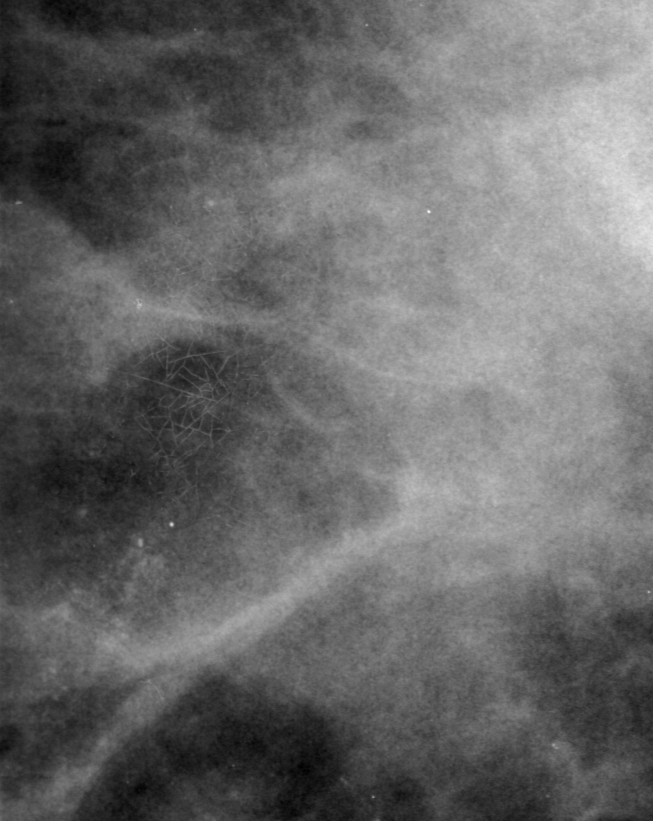
Region of interest cut from a scanned film mammogram (one marked finding); left breast; CC view; BI-RADS breast density category 3 (scale 1–4).
- Finding: calcifications, morphology fine linear branching, distribution linear; BI-RADS assessment category 3; subtlety rating 3 on a 1 (subtle) to 5 (obvious) scale; pathology result (as recorded, not read from the image): malignant.